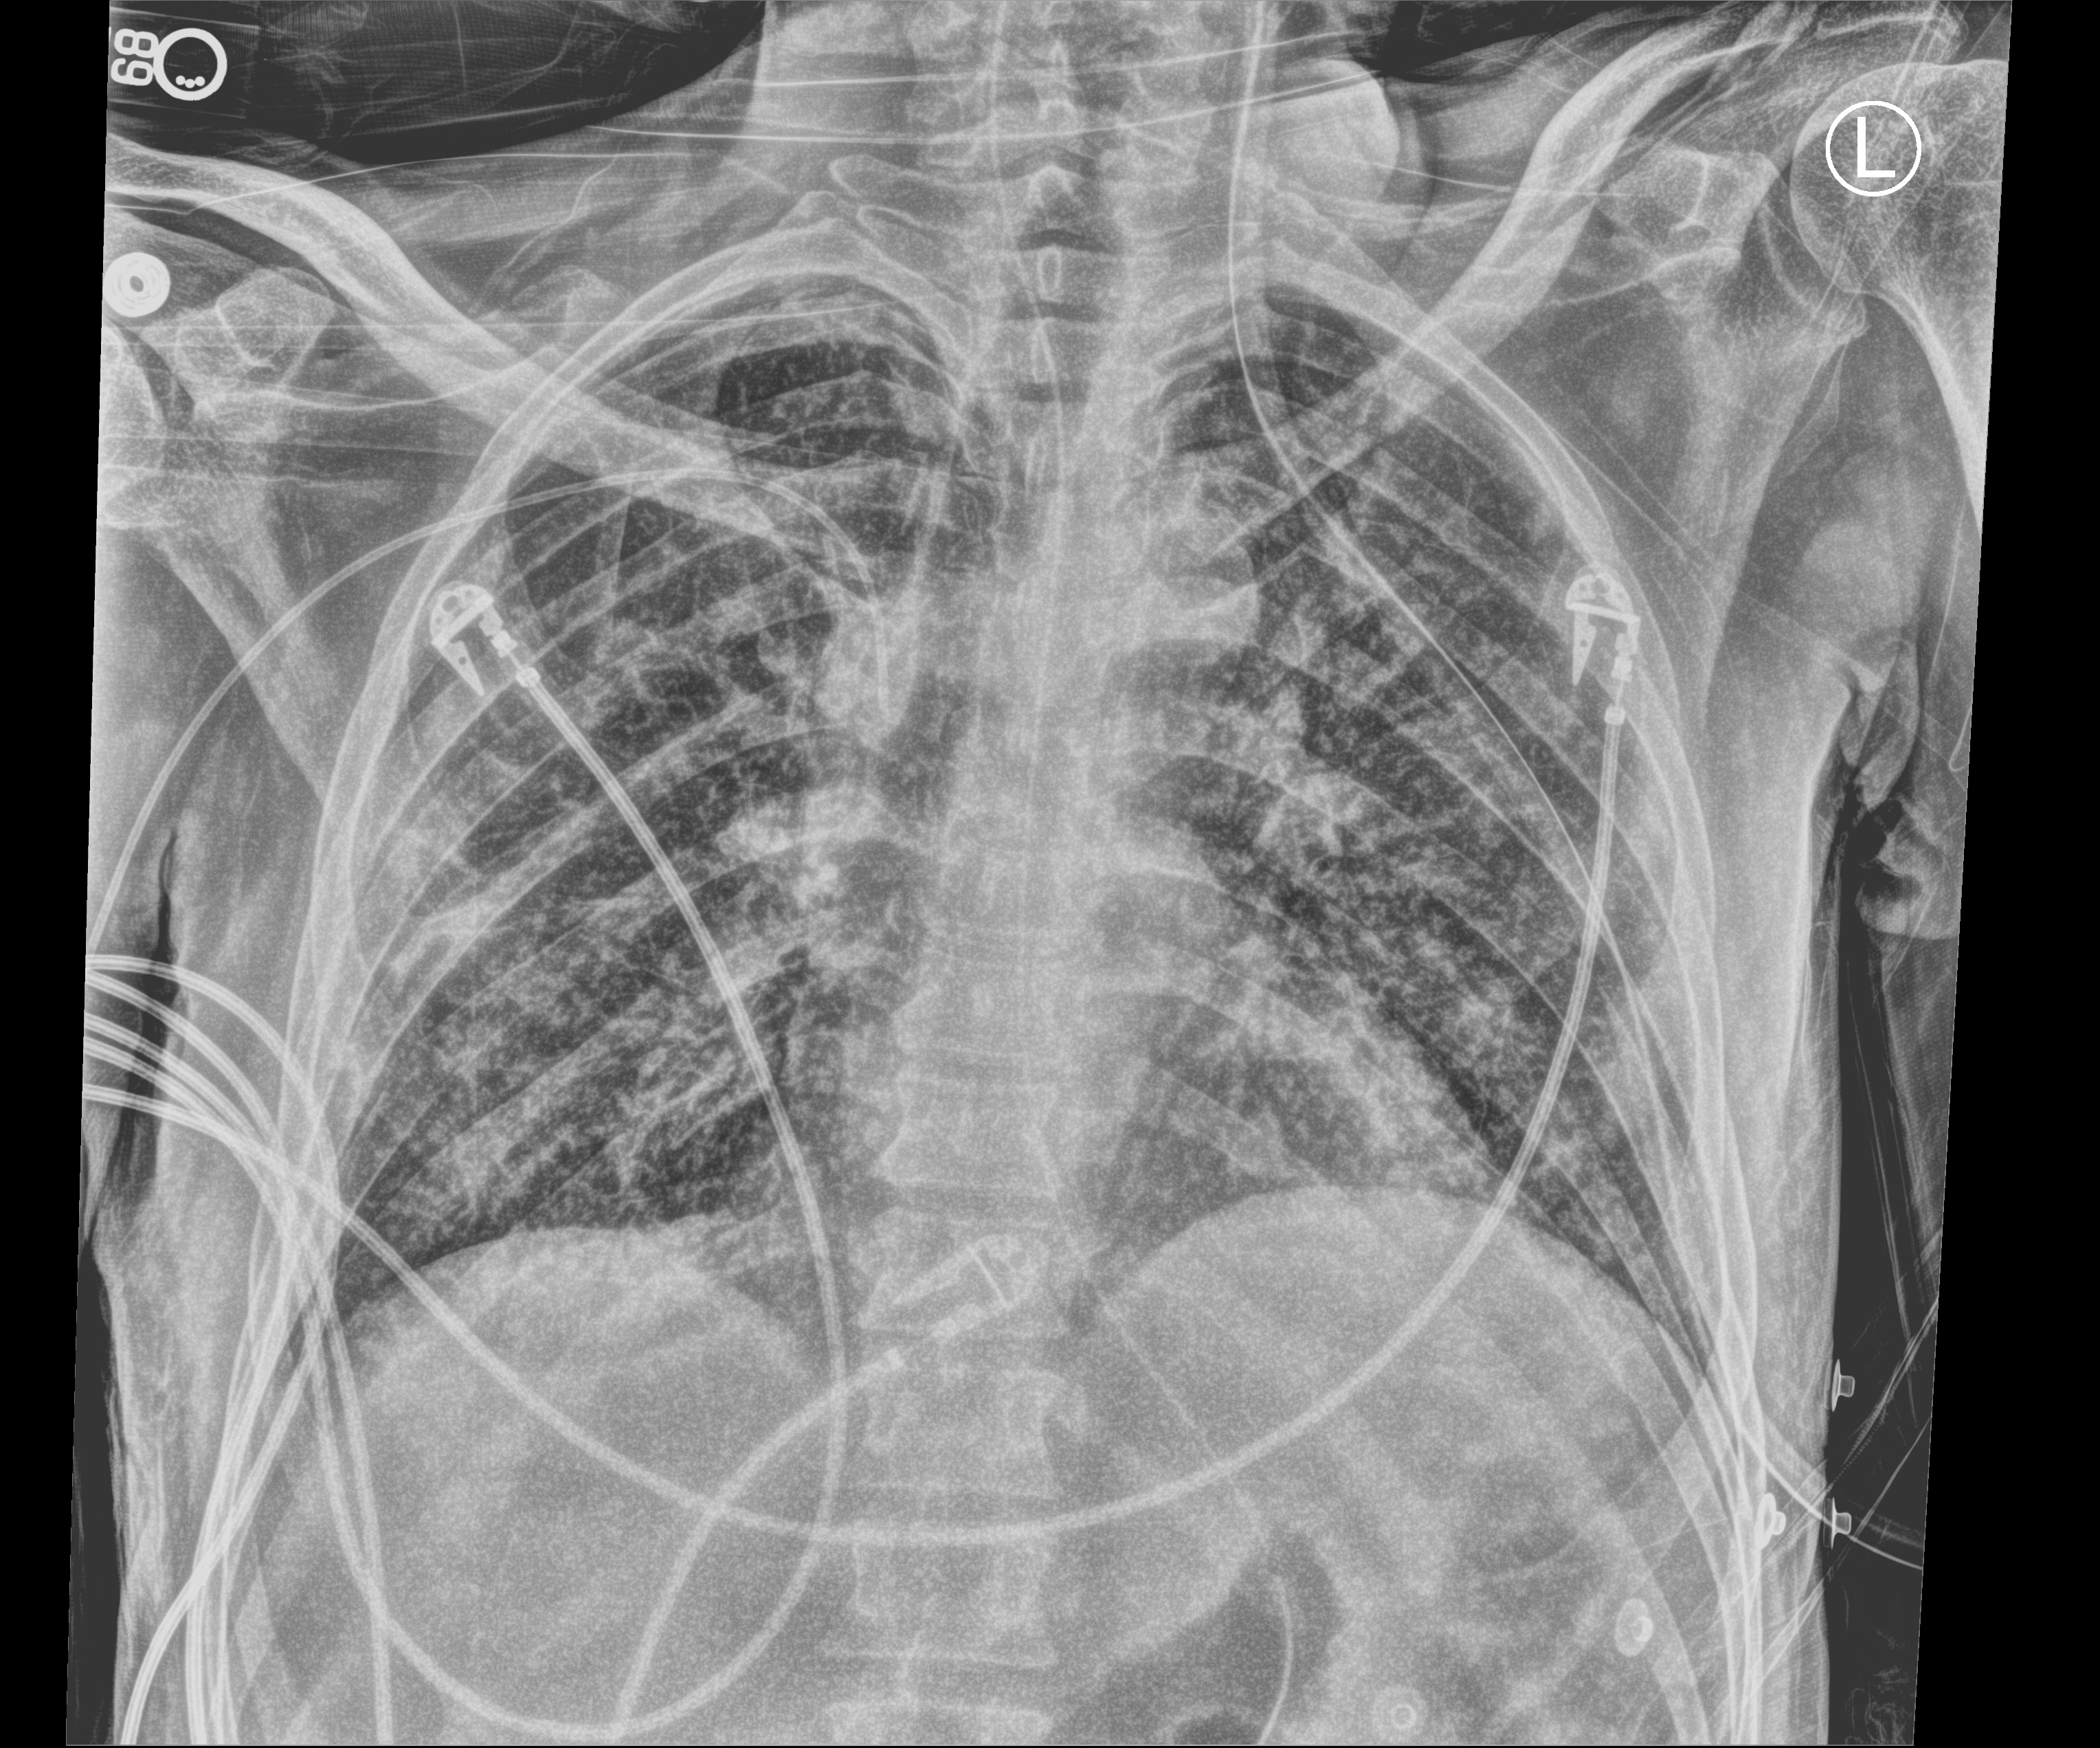
Chest X-ray (portable), anteroposterior (AP) projection. Patient hospitalised with COVID-19; male, aged 18–59 years.
Hospital-stay facts (about this admission, not read from this image; timing relative to this image not recorded): admitted to intensive care during this hospital stay: yes; mechanically ventilated during this hospital stay: yes.